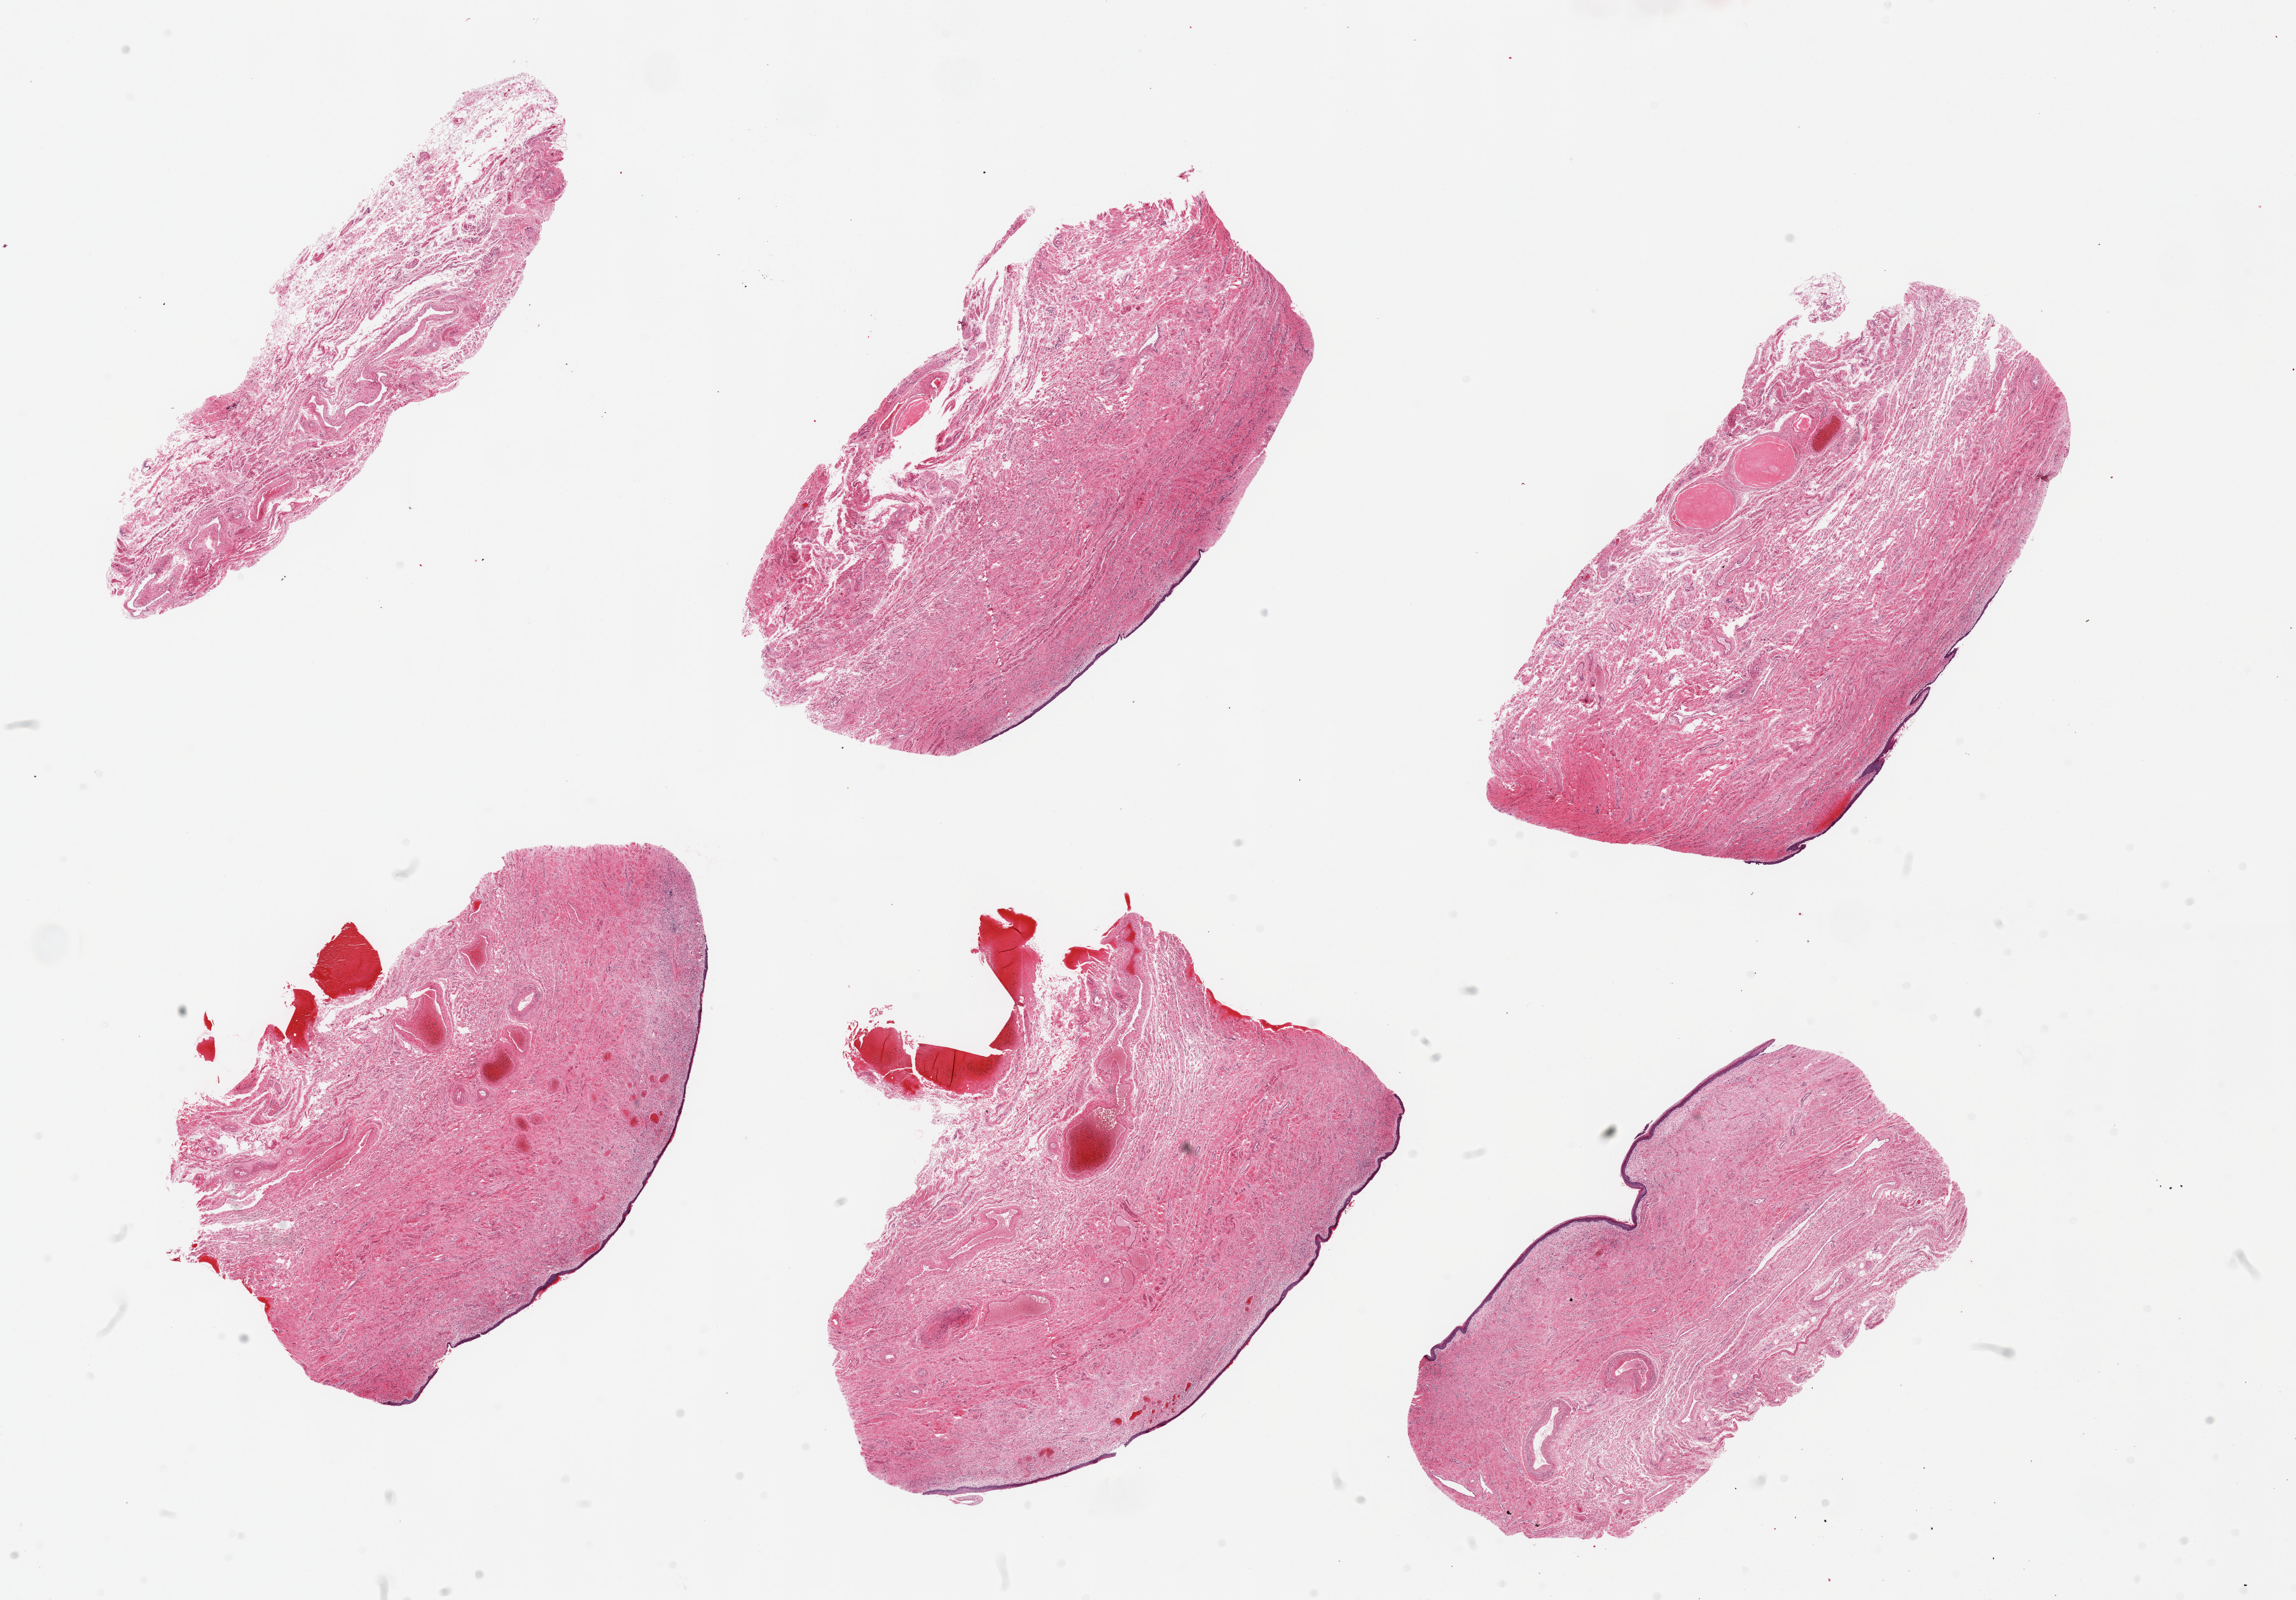
Whole-slide image, hematoxylin and eosin (H&E) stain, whole scanned area (about 28.5 x 19.9 mm) shown as a low-resolution overview. PAXgene-fixed paraffin-embedded (PFPE) section. Section of vagina (target tissue). Donor tissue sample.
Review note (as recorded): 6 pieces; atrophic, partly sloughed epithelium; 1 piece is only perivaginal stroma.